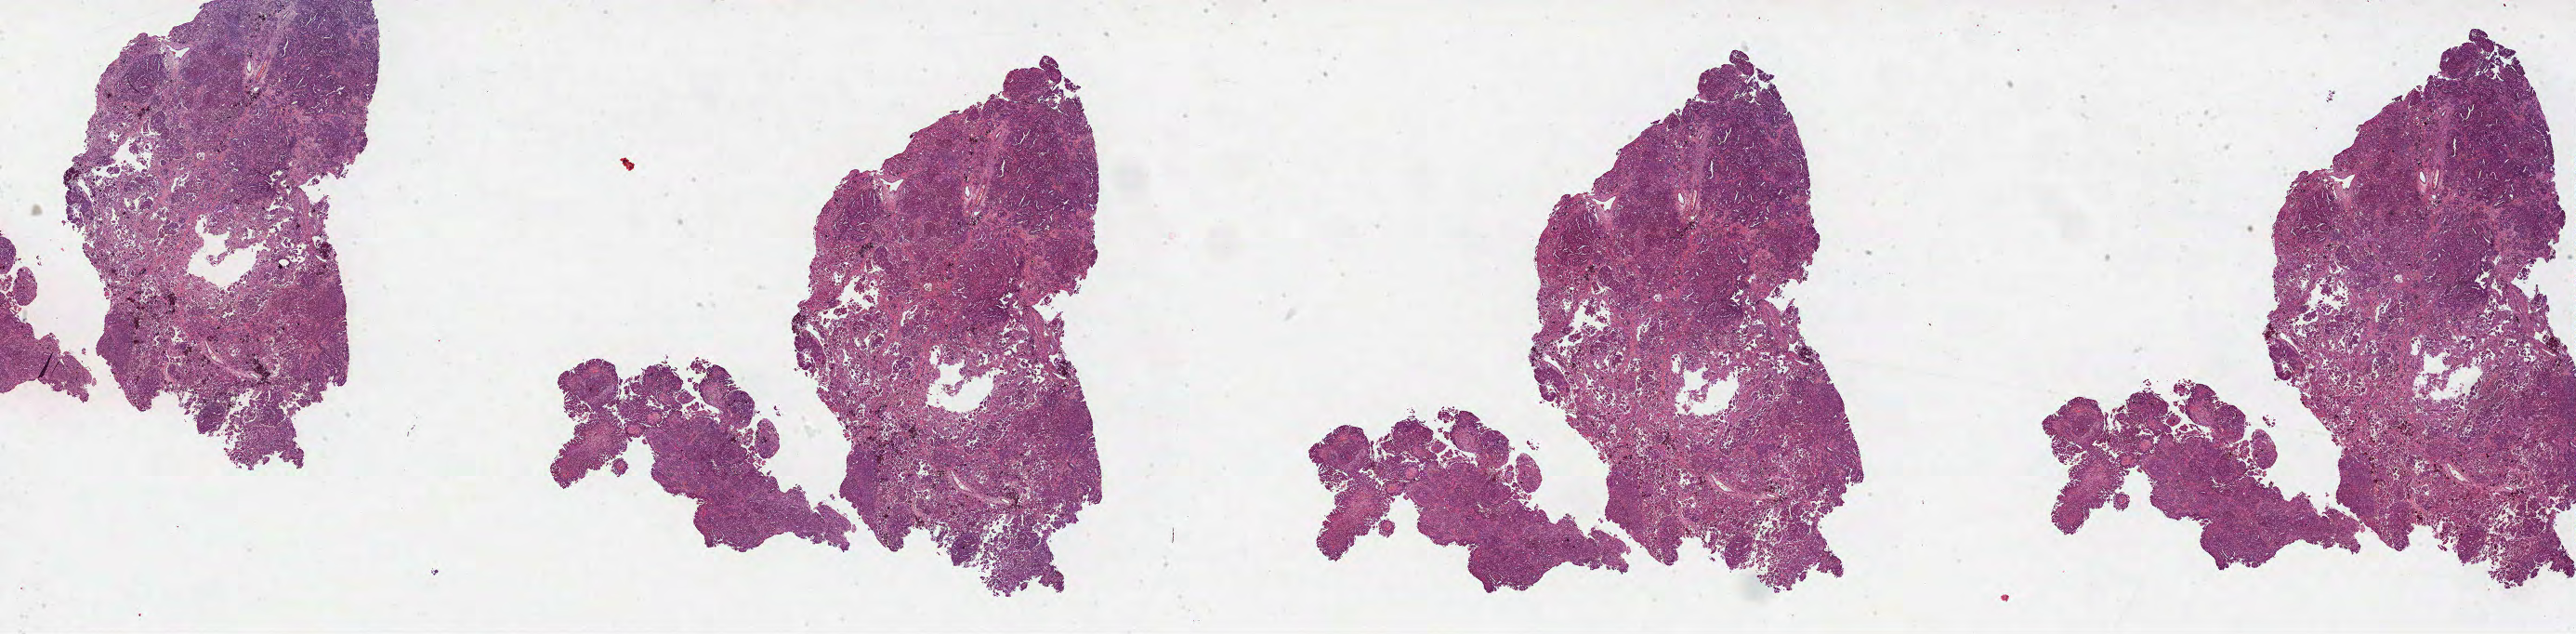
Digitized H&E-stained tissue section (whole slide), low-resolution overview of the scanned area, about 44.7 x 11.0 mm (from a 40x scan); formalin-fixed paraffin-embedded (FFPE) diagnostic section; primary tumour sample from the ovary. Patient: female, age at initial diagnosis 57 years. Histologic grade: G2 (moderately differentiated).
FIGO stage: IV. Pathologic diagnosis: Serous cystadenocarcinoma, NOS.